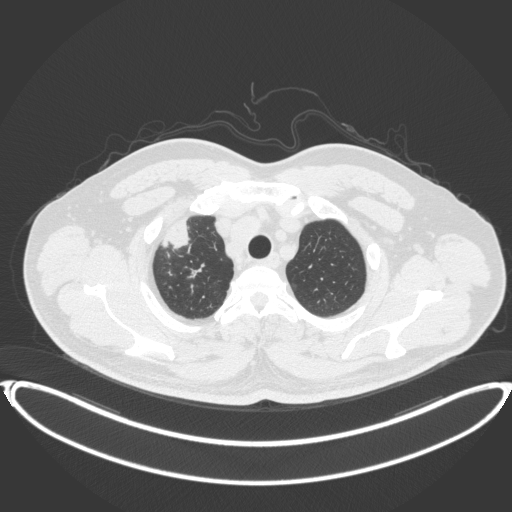
Chest CT, one axial slice. Reconstruction kernel B31f. 120 kVp. Lung window (W 1500 / L -600 HU). 1 mm slice thickness. 512 × 512 image matrix, field of view 445 × 445 mm. Male patient, age 53 years. From the clinical record (not read from this slice): clinical TNM (as recorded): T2a N0 M0.
Annotated regions visible in this slice (rectangle marked by the reading radiologist):
- lung tumour (recorded histology: adenocarcinoma): bounding box (x1, y1, x2, y2) in pixels: (162, 218, 197, 253)